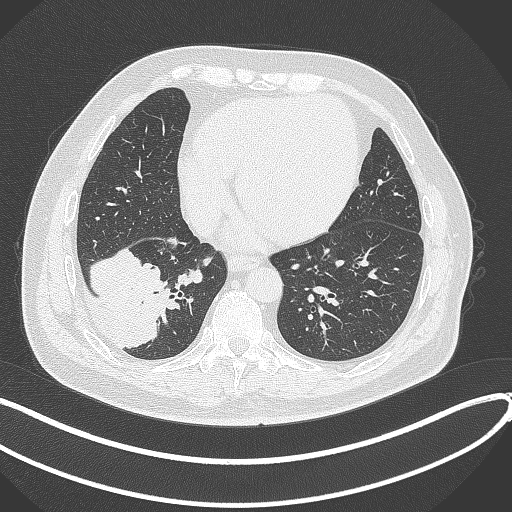
Chest CT, one axial slice. Slice 117 of 360 in the series (ordered by position). 120 kVp. Lung window (W 1500 / L -600 HU). 512 × 512 image matrix, field of view 400 × 400 mm. Patient: male, 59 years.
Outlined on this slice (bounding box drawn by a radiologist):
- lung tumour (recorded histology: adenocarcinoma): box from (x=85, y=240) to (x=181, y=347) px